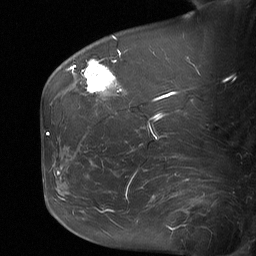
Breast MRI (dynamic contrast-enhanced), one sagittal slice; position 21 of 64 along the scan axis; dynamic contrast-enhanced study with each time point stored as its own series, time point 2 of 3 at this slice position (early post-contrast, ordered by acquisition time); 1.5 T; TE 4.8 ms, TR 27 ms; 2 mm slice thickness; 256 × 256 image matrix. Female patient, age 60 years. From the clinical record (not read from this slice): setting: breast cancer imaged before/during neoadjuvant chemotherapy; receptor status: HR-positive, HER2-negative.
Annotated regions visible in this slice (semi-automatic segmentation, software-assisted and operator-edited):
- analysis volume of interest (the breast-tissue region the enhancement analysis was run in; not a lesion): bounding box <79,50,122,99> (left, top, right, bottom; pixels)
- tumour enhancement mask (voxels above the 90 % enhancement threshold inside the analysis volume of interest): <85,59,115,93>